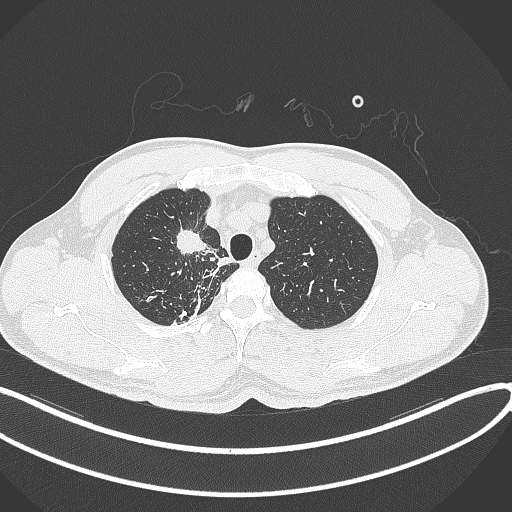
Chest CT, one axial slice; slice 312 of 391 in the series (ordered by position); reconstruction kernel B70f; 120 kVp; lung window (W 1500 / L -600 HU); 1 mm slice thickness; 512 × 512 image matrix, field of view 400 × 400 mm. Patient: male, 48 years. Case-level facts recorded for this patient, not image findings: clinical TNM (as recorded): T1c N1 M1.
Structures marked on this image (rectangle marked by the reading radiologist):
- lung tumour (recorded histology: adenocarcinoma): bounding box [x1, y1, x2, y2] px = [170, 224, 211, 262]